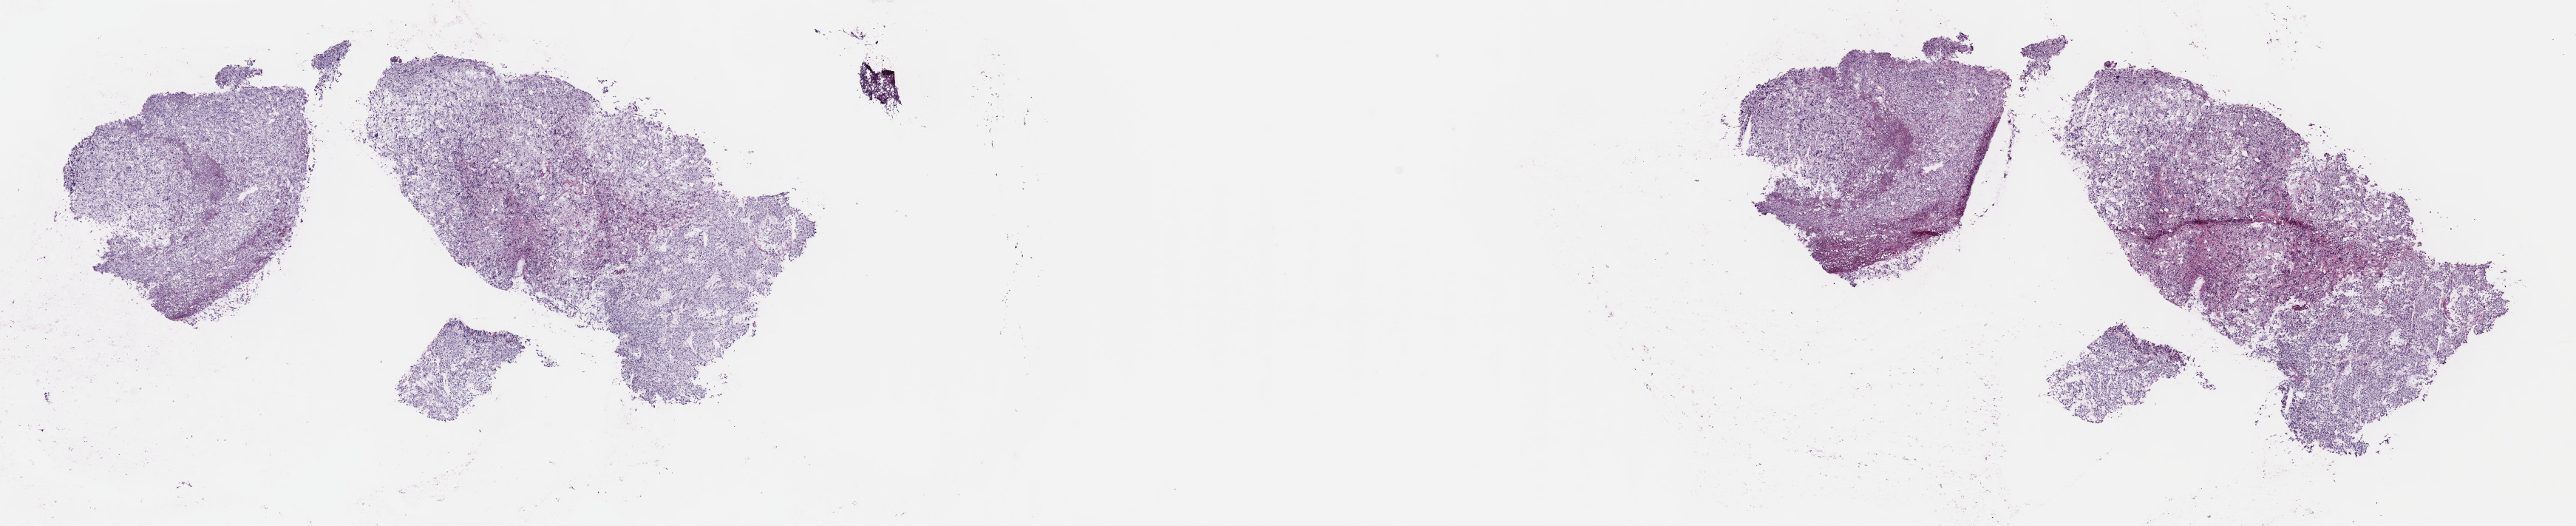
Hematoxylin and eosin (H&E) stained whole-slide image, shown as a low-resolution overview of the whole scanned area (about 28.2 x 5.8 mm, from a 40x scan). Frozen section. Adrenal gland, primary tumour sample. Male, age 80 years at initial diagnosis. Pathologist review of this section (percent, as recorded): tumour cells 80%, tumour nuclei 80%, normal cells 0%, stromal cells 20%, necrosis 0%. Infiltration values recorded for this section: lymphocyte infiltration 2%, monocyte infiltration 1%, neutrophil infiltration 1%.
Histologic diagnosis: Pheochromocytoma, NOS.